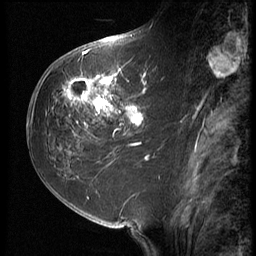
Breast MRI (dynamic contrast-enhanced), one sagittal slice. Position 28 of 64 along the scan axis. 3 images stored at this slice position (order not interpretable as contrast timing). 1.5 T. TE 4.2 ms, TR 9 ms. 2.5 mm slice thickness. 256 × 256 image matrix, field of view 180 × 180 mm. Female patient, age 59 years. From the clinical record (not read from this slice): setting: breast cancer imaged before/during neoadjuvant chemotherapy; receptor status: HER2-positive.
Annotated regions visible in this slice (semi-automatically segmented with operator editing):
- analysis volume of interest (the breast-tissue region the enhancement analysis was run in; not a lesion): bounding box [x1, y1, x2, y2] px = [54, 65, 155, 132]
- tumour enhancement mask (voxels above the 140 % enhancement threshold inside the analysis volume of interest): [62, 65, 149, 131]